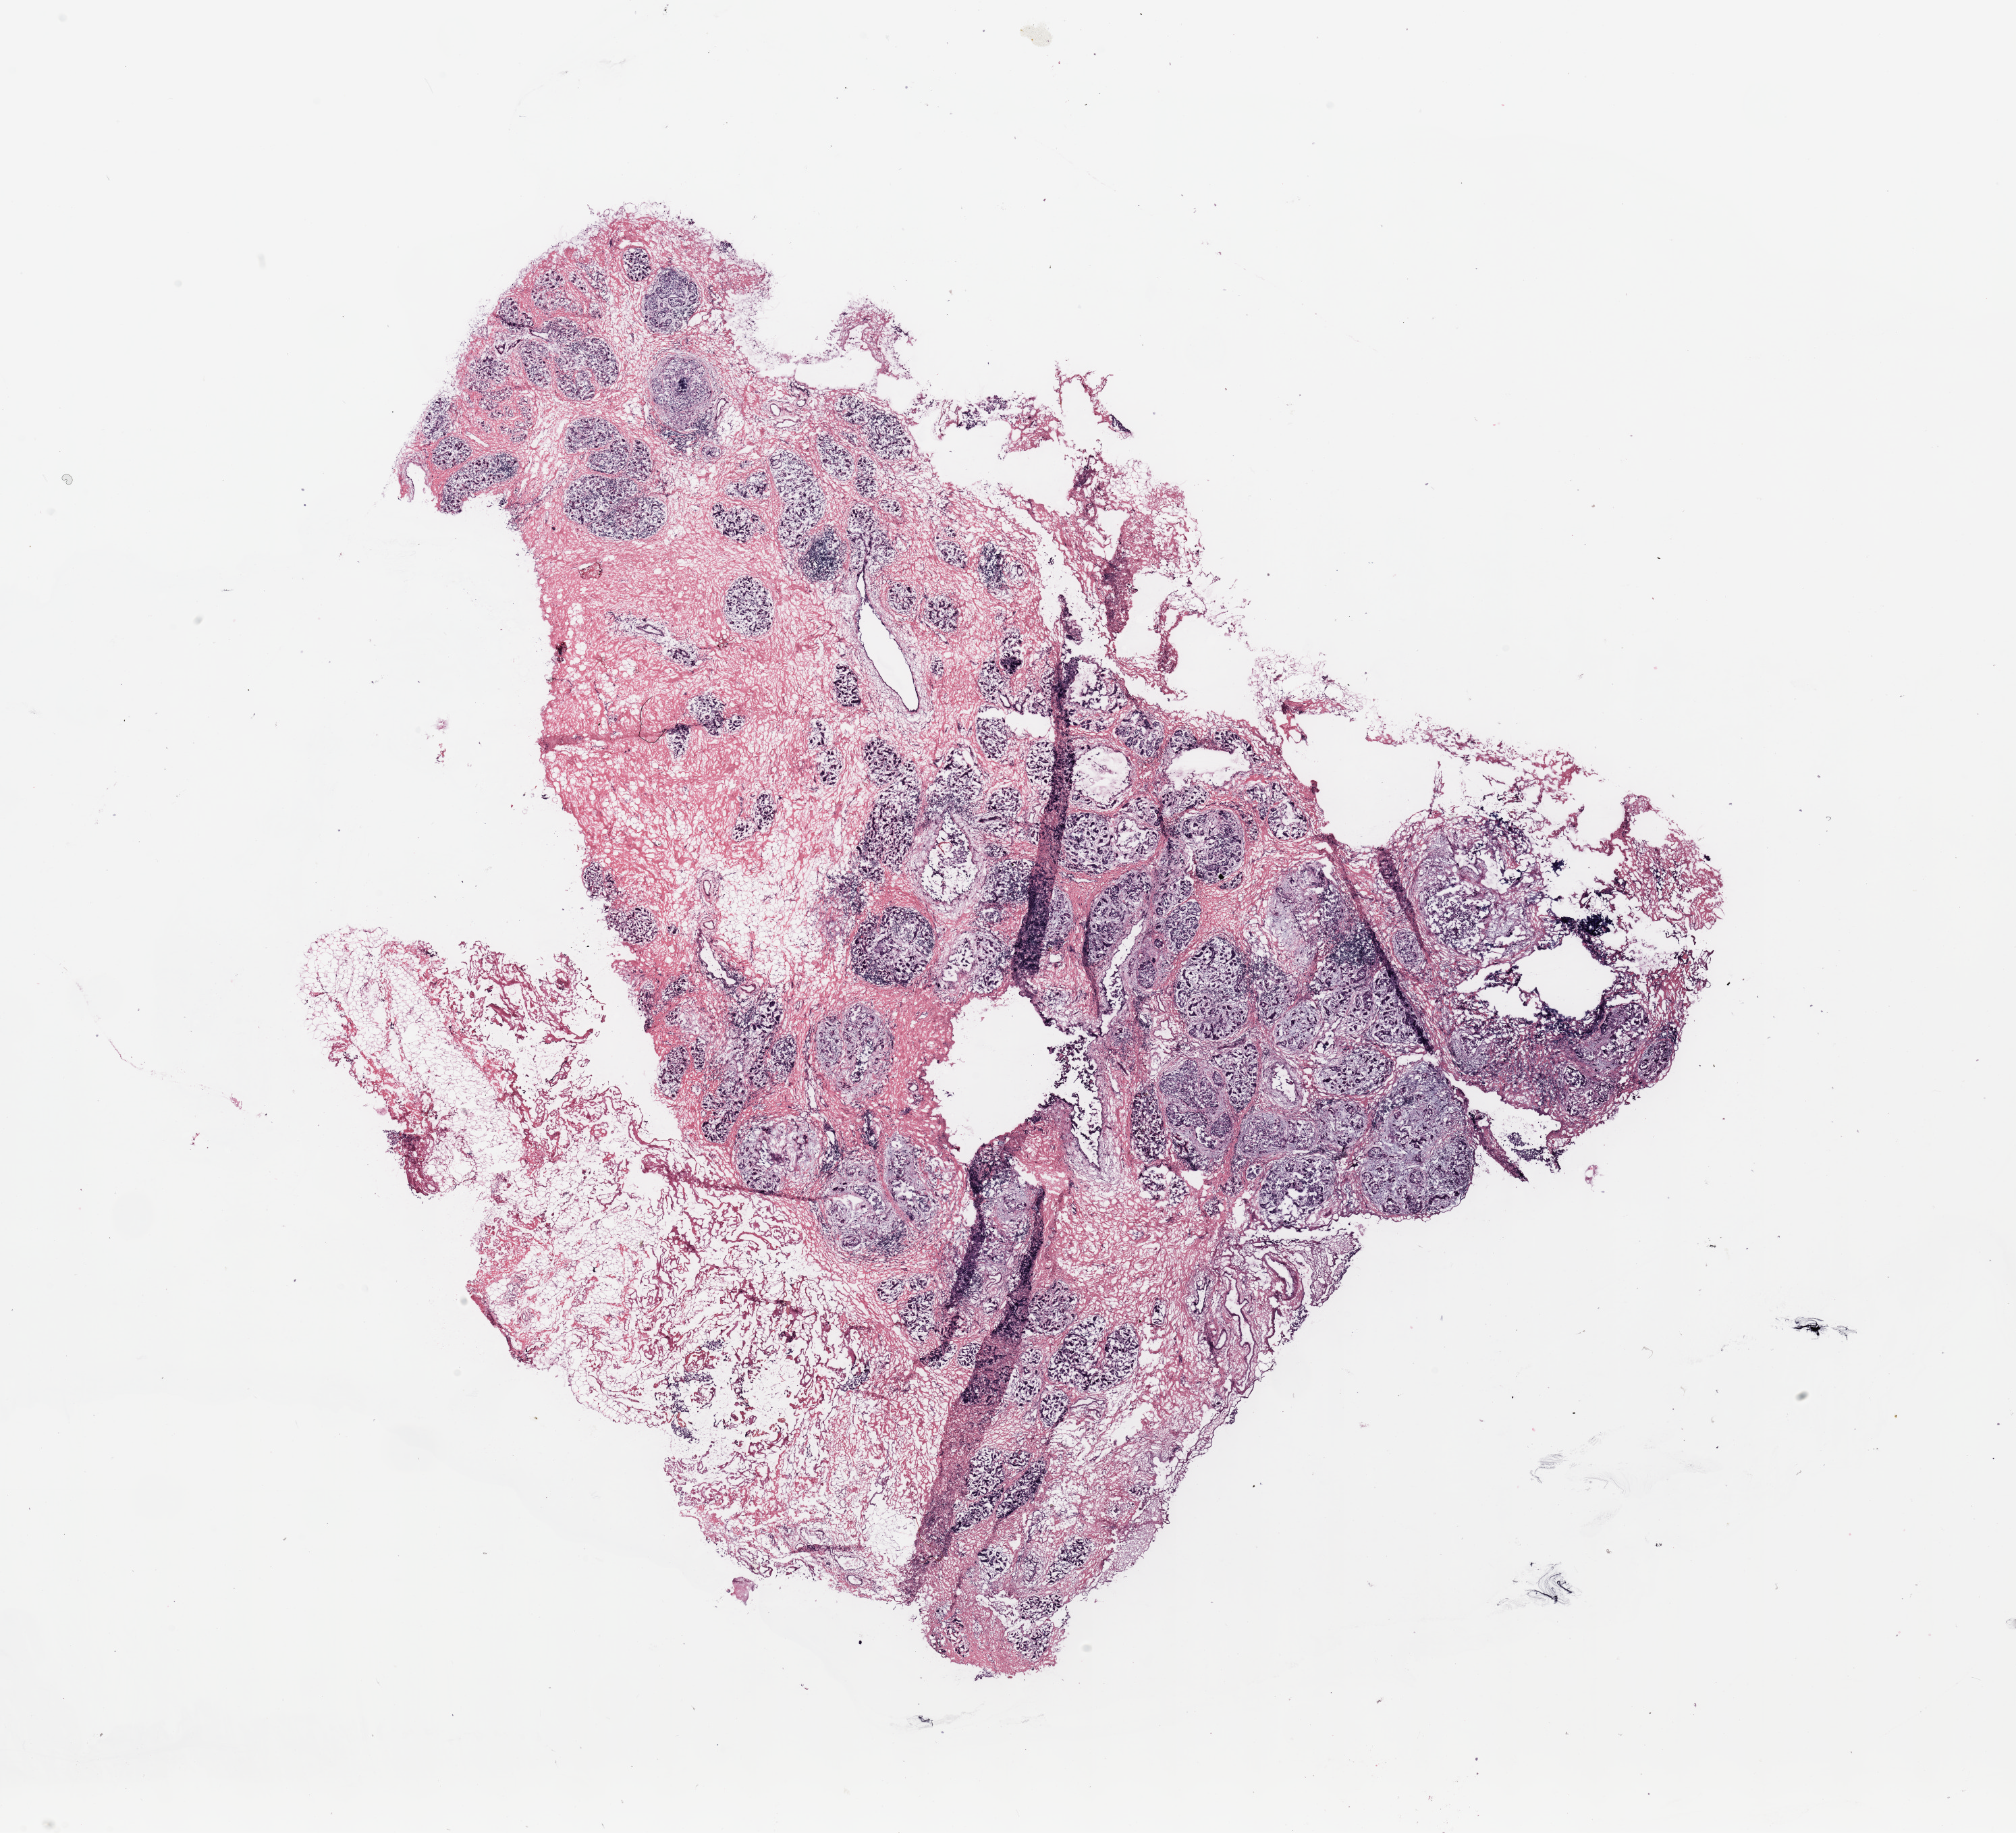
Digitized H&E tissue section (whole slide), shown as a low-resolution overview of the whole scanned area (about 23.6 x 21.5 mm, acquisition: 20x scan). Breast, tissue type not recorded.
Patient diagnosis (cohort enrolment): breast cancer (breast).